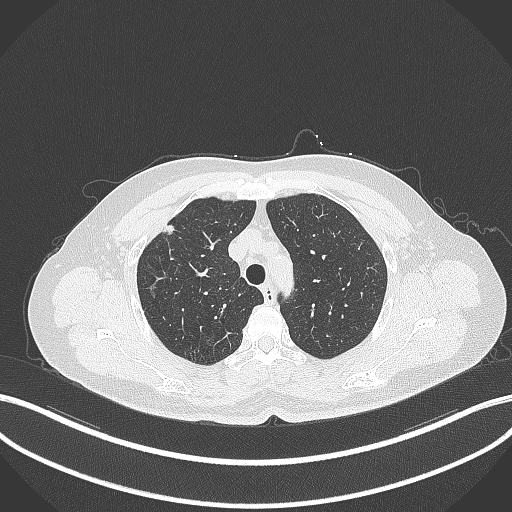
Chest CT, one axial slice. Reconstruction kernel B70f. Lung window (W 1500 / L -600 HU). 1 mm slice thickness. 512 × 512 image matrix, field of view 400 × 400 mm. Female patient, age 56 years. Case-level facts recorded for this patient, not image findings: clinical TNM (as recorded): T1c N0 M0.
Annotated regions visible in this slice (rectangle marked by the reading radiologist):
- lung tumour (recorded histology: adenocarcinoma): bounding box [x1, y1, x2, y2] px = [159, 222, 178, 238]